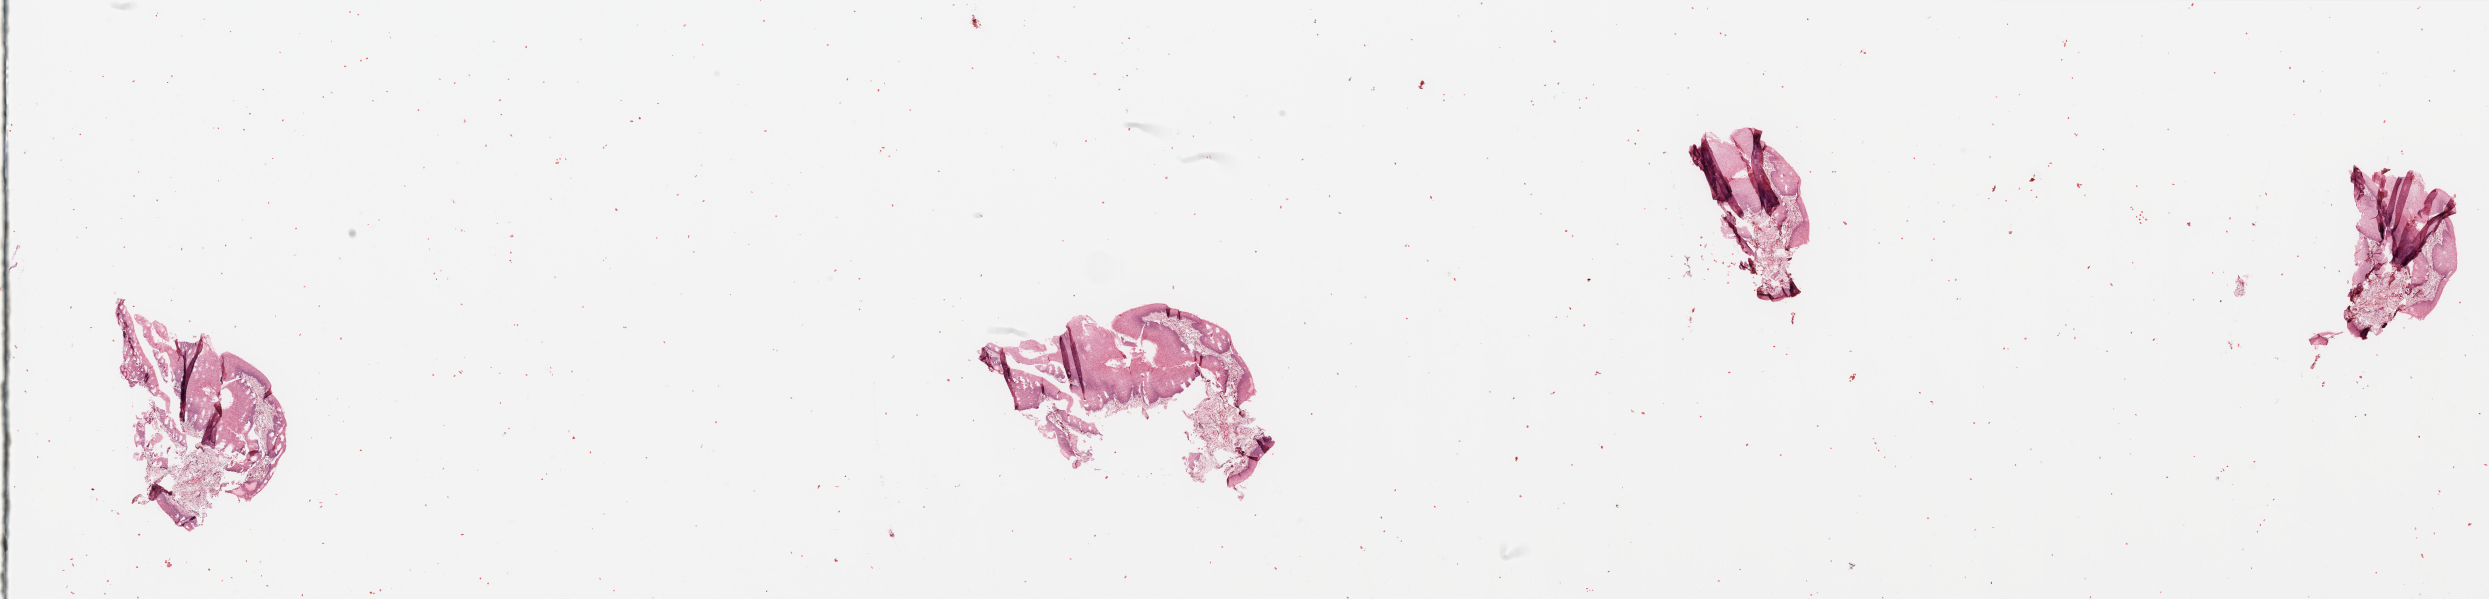
Digitized H&E-stained tissue section (whole slide), shown as a low-resolution overview of the whole scanned area (about 39.4 x 9.5 mm, from a 20x scan), normal (non-tumour) tissue sample, sampled site: larynx. Patient: male, age 64 years.
This section: normal (non-tumour) tissue from the same patient. Patient diagnosis: Squamous cell carcinoma, NOS (larynx, NOS).